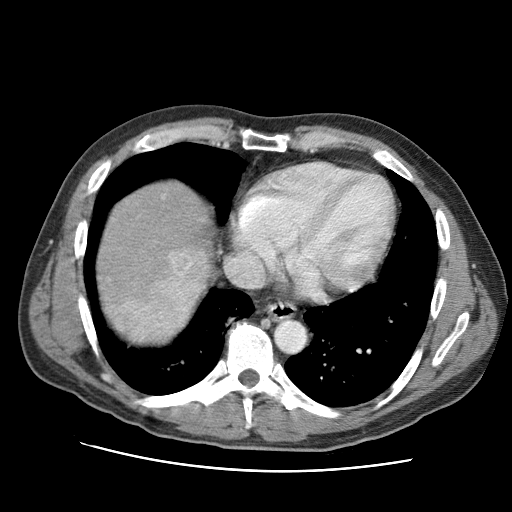
Contrast-enhanced abdominal CT (liver protocol), one axial slice. Position 87 of 95 along the scan axis. Reconstruction kernel STANDARD. One of 2 acquisitions stored at this slice position. Soft-tissue window (W 400 / L 40 HU). 512 × 512 image matrix, field of view 360 × 360 mm. Case-level facts recorded for this patient, not image findings: diagnosis: hepatocellular carcinoma (patient treated with transarterial chemoembolisation; whether this scan precedes or follows treatment is not stated here); TNM stage (as recorded): Stage-IVA; Child-Pugh class: A; tumour differentiation: moderately differentiated; tumour nodularity: multinodular.
Annotated regions visible in this slice (semi-automatically segmented with operator editing):
- liver parenchyma outside the tumour (the mass and vessels are separate outlines, so this box may not span the whole liver): box from (x=98, y=182) to (x=212, y=342) px
- mass: (x=119, y=248)–(x=210, y=341)
- liver vessels: (x=169, y=253)–(x=173, y=257)